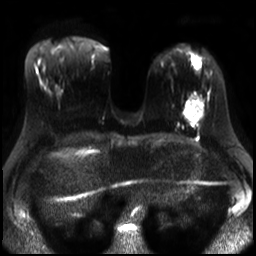
Breast MRI, one axial slice; position 9 of 30 along the scan axis; diffusion-weighted series; image 2 of 4 stored at this slice position (different b-values; order by instance number); 3 T; 256 × 256 image matrix, field of view 320 × 320 mm. Female patient.
Outlined on this slice (manually delineated by an expert):
- tumour on diffusion-weighted imaging: bounding box [x1, y1, x2, y2] px = [185, 96, 203, 123]